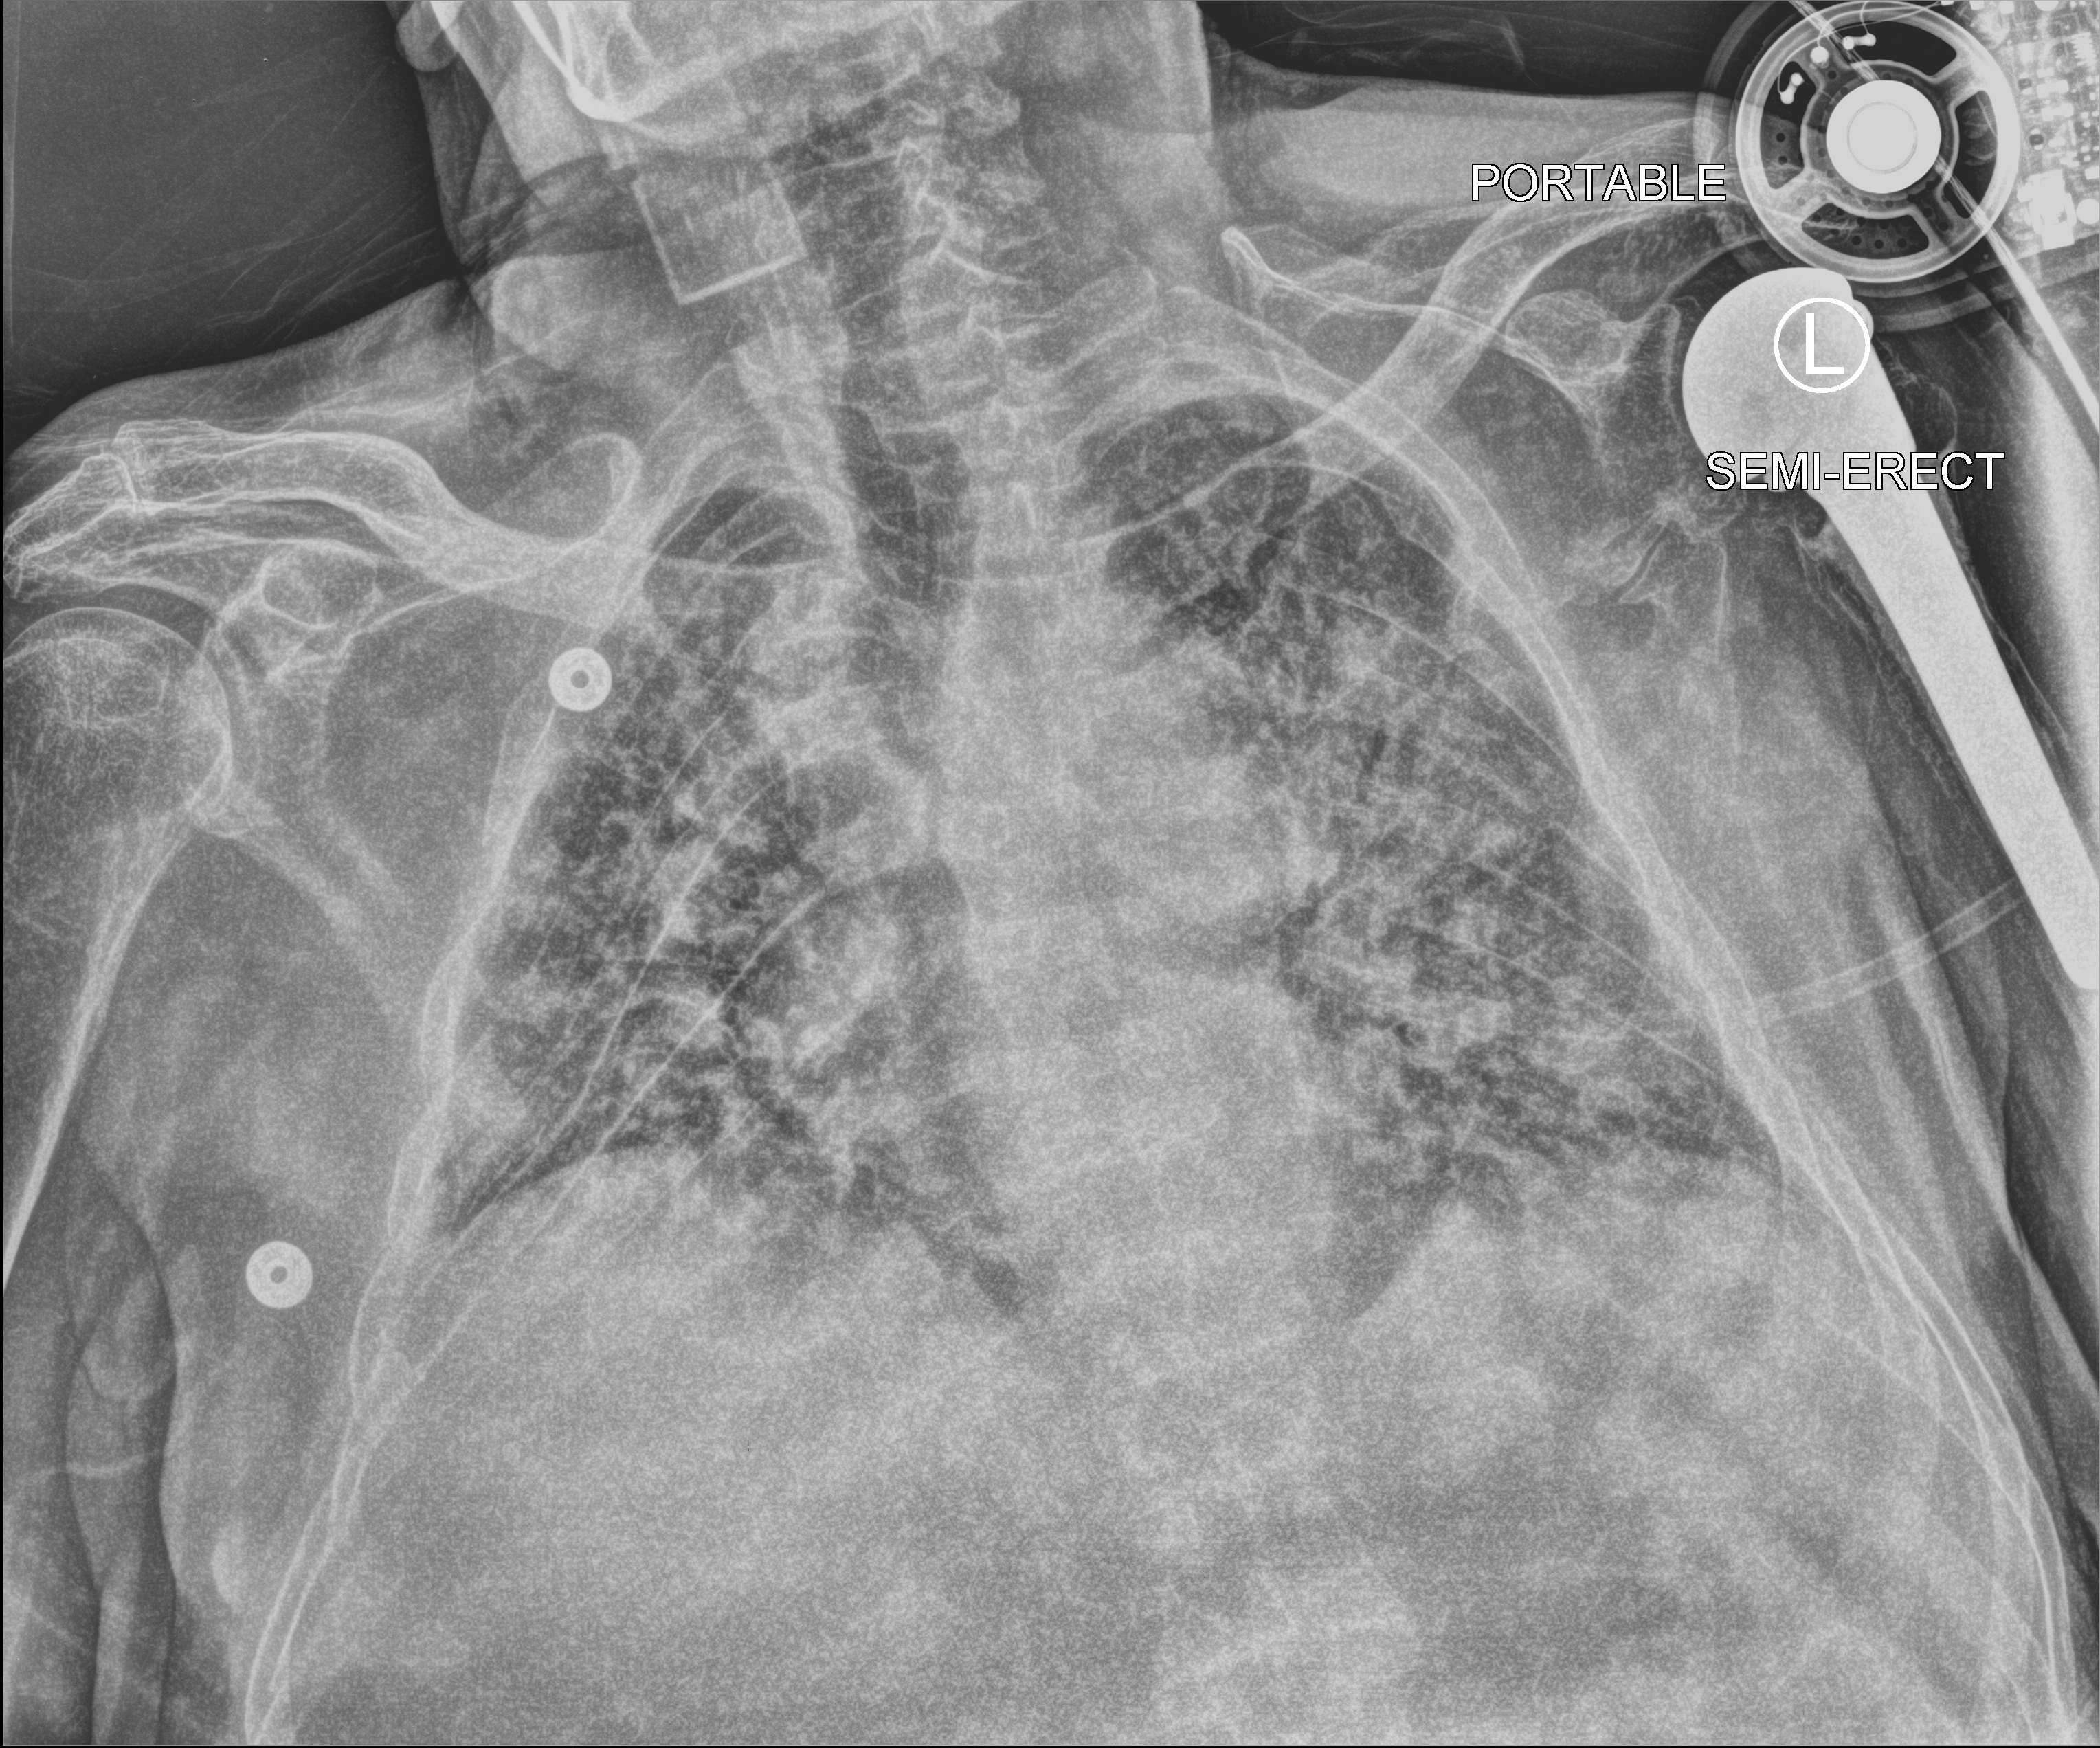
Bedside chest radiograph (computed radiography). Patient hospitalised with COVID-19; male, aged 60–74 years.
From the hospital-stay record, not from the radiograph (when in the stay this image was taken is not recorded): admitted to intensive care during this hospital stay: no; COPD (admission record): no; smoking status (admission record): never.